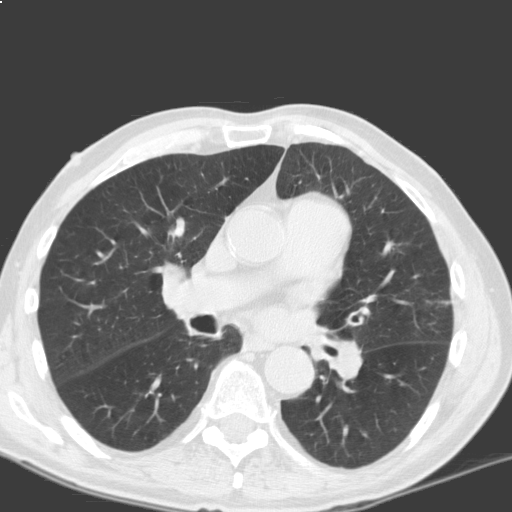
Chest CT (low-dose screening protocol), one axial image. First (baseline) screen. Lung window (W 1500 / L -600 HU). Male participant, aged 69 years at enrolment. Current smoker at enrolment.
- Lesion marked by an expert reader, bounding box <145,208,208,256> (left, top, right, bottom; pixels).
- Reader record for this screening exam (exam-level; its link to the box is not recorded): non-calcified nodule or mass ≥4 mm, left lower lobe, 5 × 5 mm, smooth margins, soft tissue attenuation.
- Note: the box lies in the patient's right hemithorax on this image, whereas the reader's record names the left lung; they may be different findings.
- Participant outcome: lung cancer diagnosed 317 days after this screen — squamous cell carcinoma, NOS, right upper lobe, moderately differentiated (G2), stage IB (AJCC 6th edition), 40 mm at pathology.